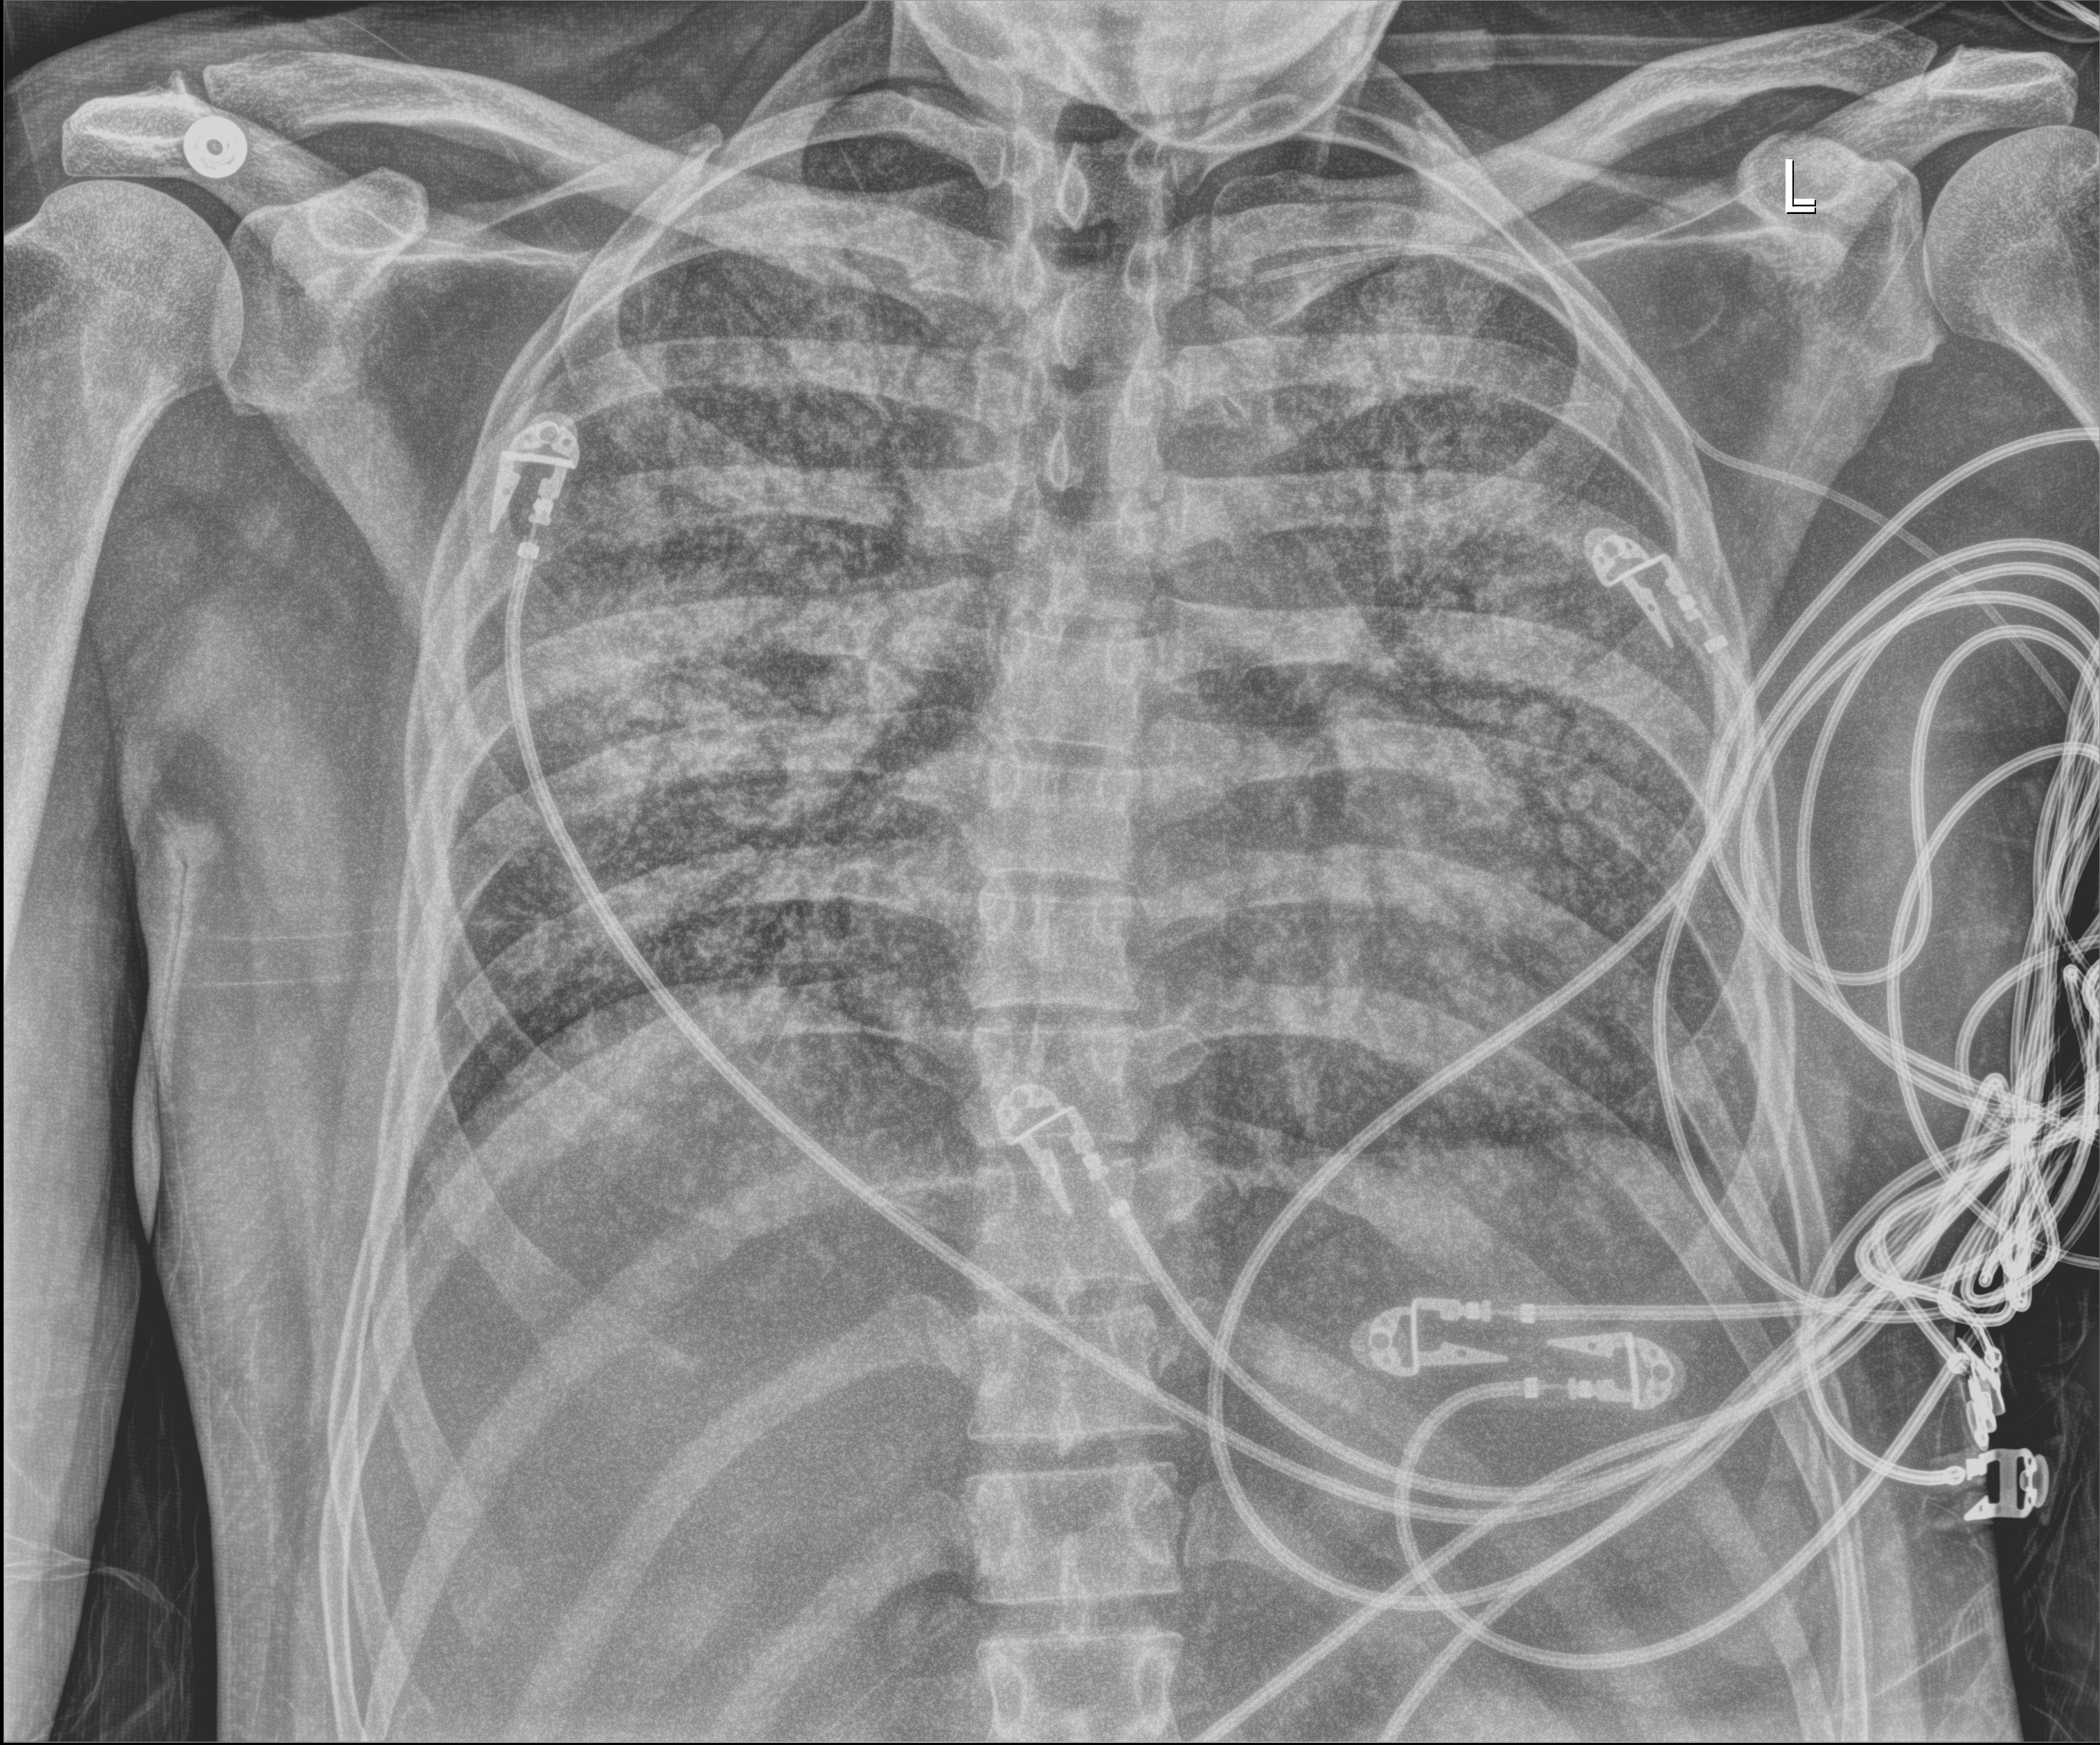
Portable chest radiograph. Patient hospitalised with COVID-19; male, aged 18–59 years.
From the hospital-stay record, not from the radiograph (when in the stay this image was taken is not recorded):
- other chronic lung disease (admission record): no